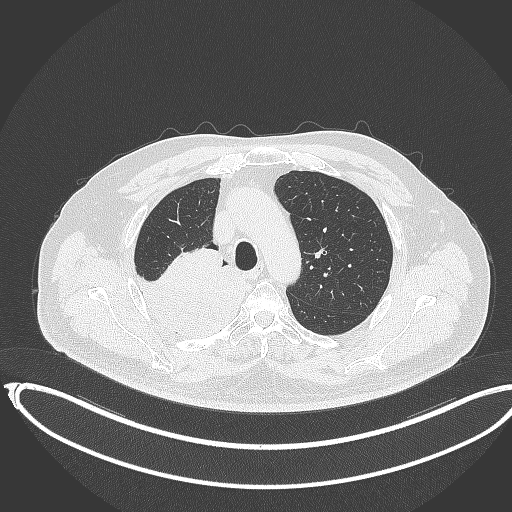
Chest CT, one axial slice. Position 272 of 403 along the scan axis. Reconstruction kernel B70f. 120 kVp. Lung window (W 1500 / L -600 HU). 1 mm slice thickness. 512 × 512 image matrix, field of view 436 × 436 mm. Patient: male, 68 years. Case-level facts recorded for this patient, not image findings: clinical TNM (as recorded): T2a N0 M0.
Outlined on this slice (rectangle marked by the reading radiologist):
- lung tumour (recorded histology: adenocarcinoma): bounding box <139,255,241,343> (left, top, right, bottom; pixels)